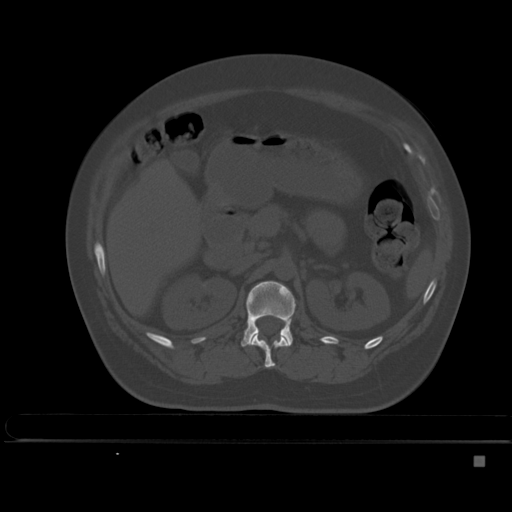
CT including the spine, one axial slice; position 202 of 495 along the scan axis; bone window (W 1800 / L 400 HU); 1.5 mm slice thickness; 512 × 512 image matrix, field of view 404 × 404 mm. Female patient, age 33 years. From the clinical record (not read from this slice): primary cancer: breast.
Outlined on this slice (semi-automatically segmented with operator editing):
- L1 vertebra: bounding box (x1, y1, x2, y2) in pixels: (241, 281, 296, 347)
- T12 vertebra: (249, 333, 290, 368)